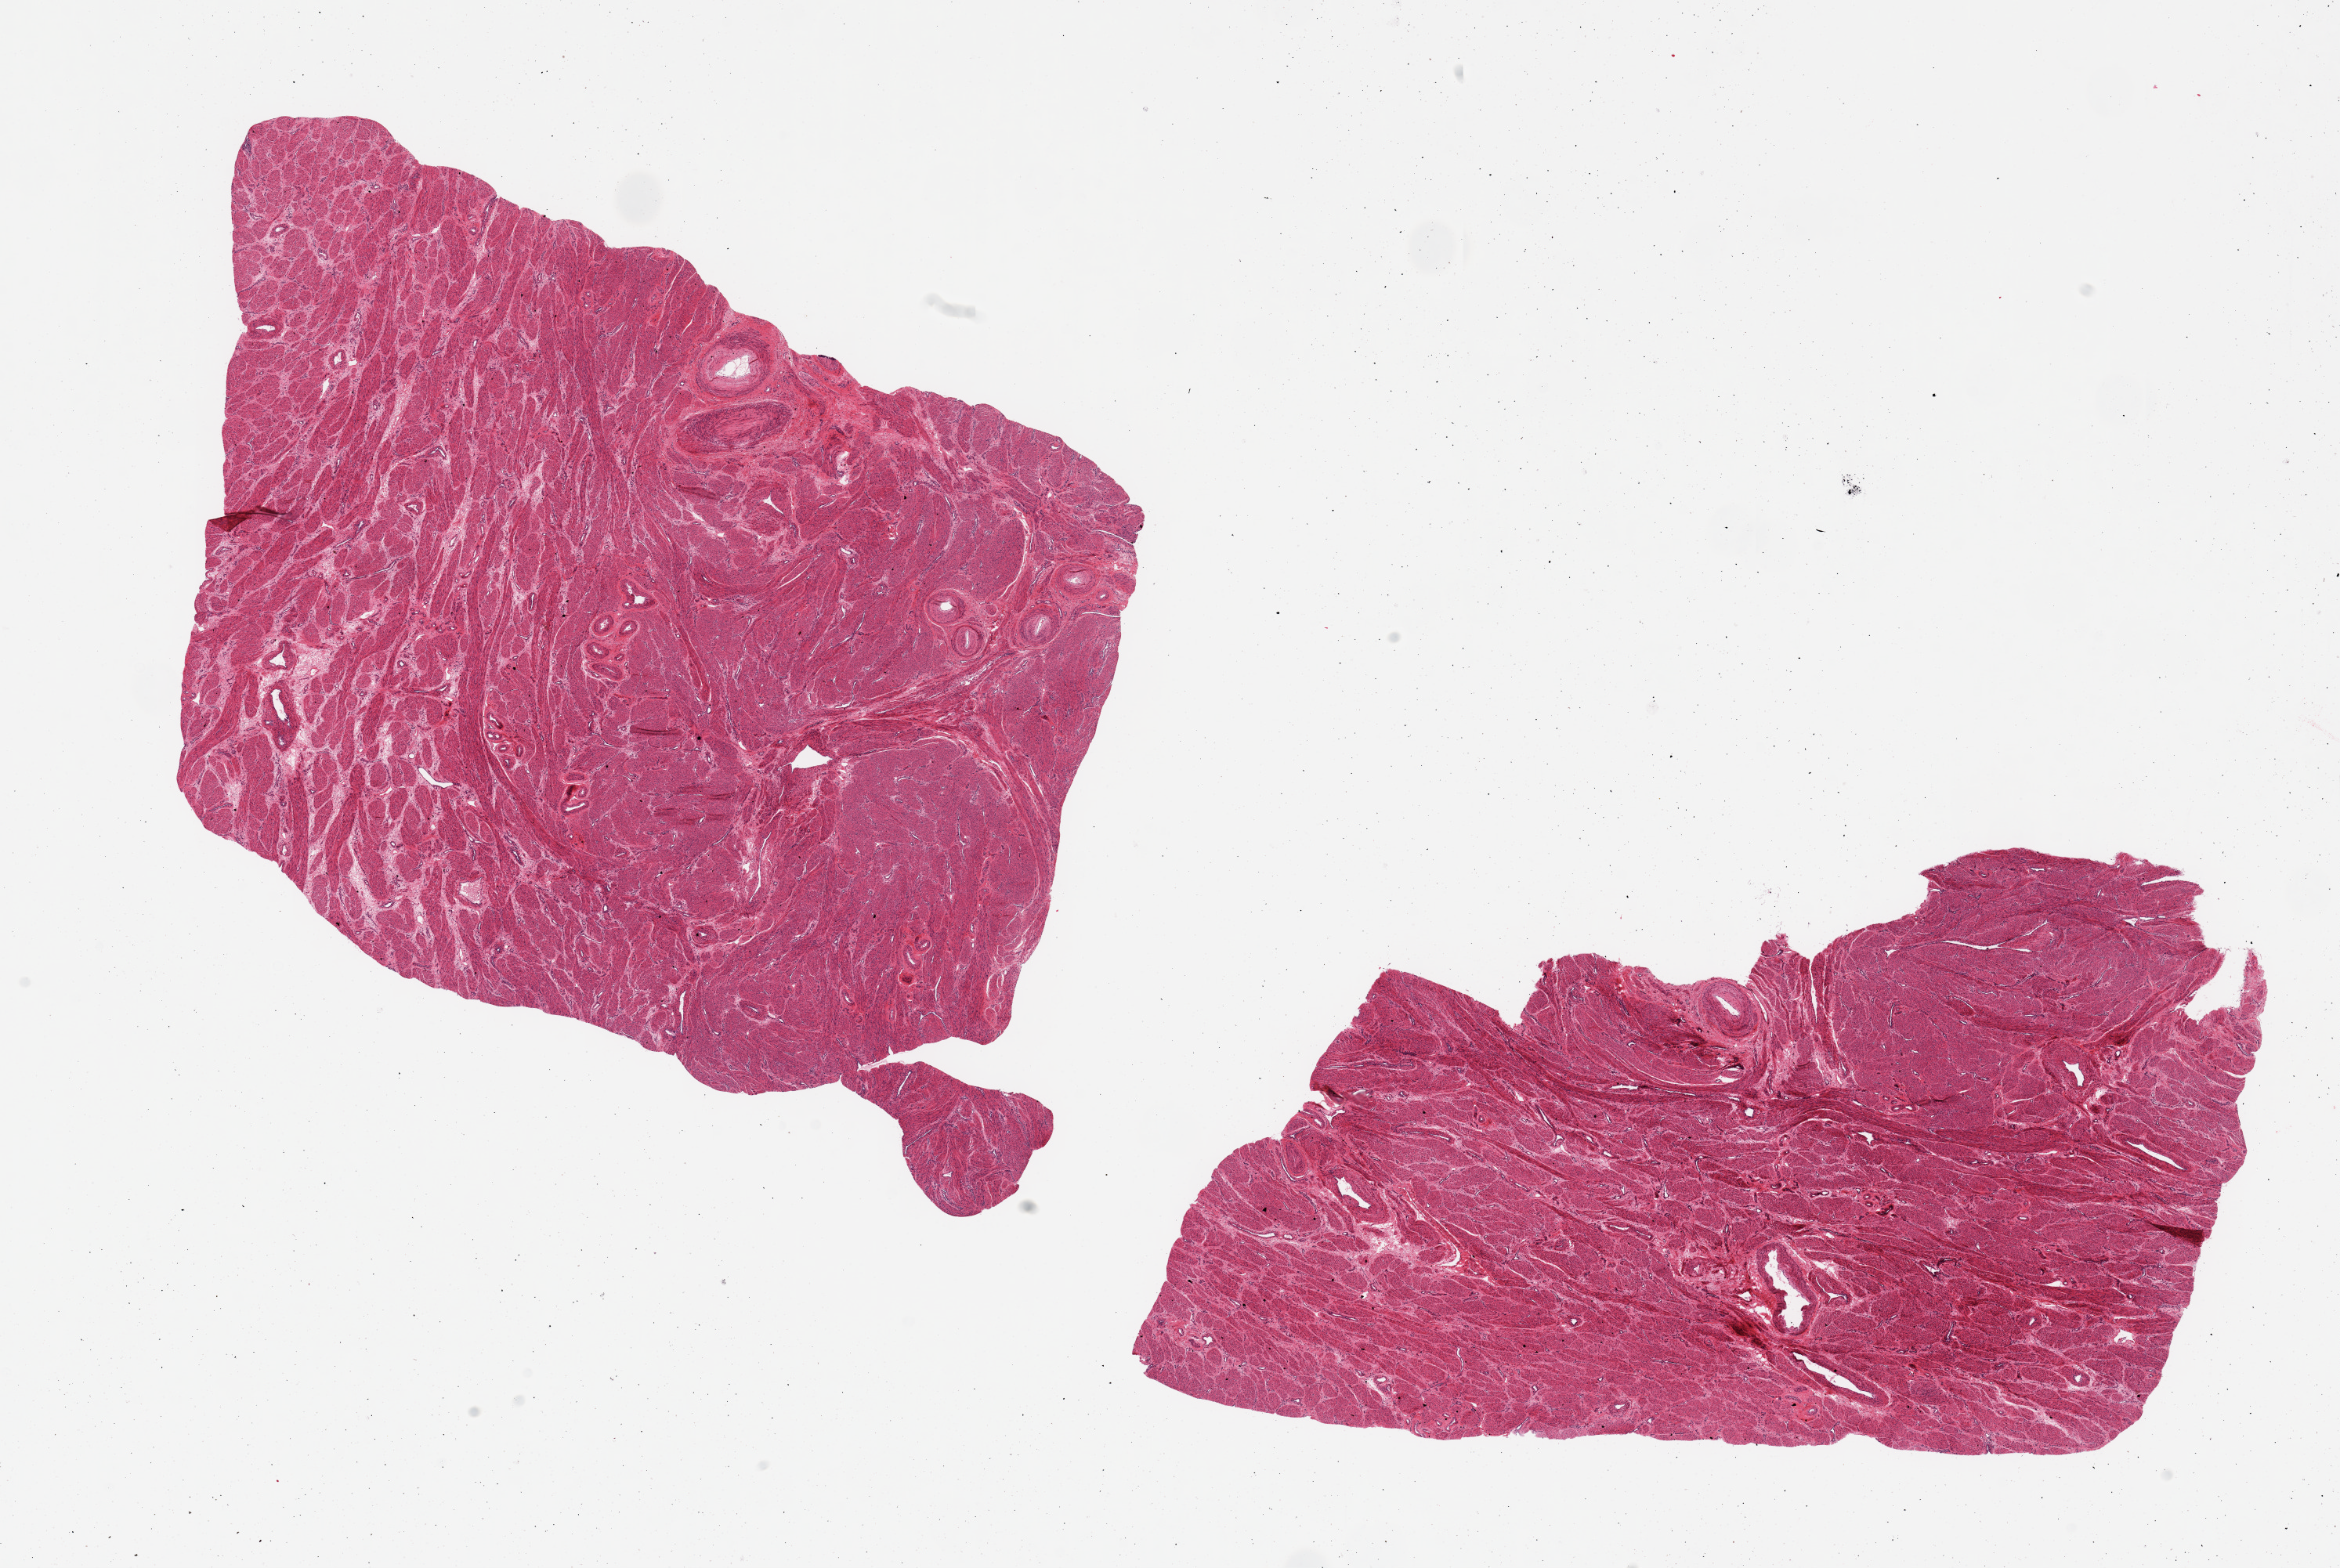
H&E whole-slide image, low-resolution overview of the scanned area, about 23.6 x 15.8 mm (from a 20x scan), PAXgene-fixed, paraffin-embedded tissue, sampled site (target tissue): uterus, tissue donor sample. Donor sex: female.
- review note (as recorded): 2 pieces, all myometrium; no abnormalities